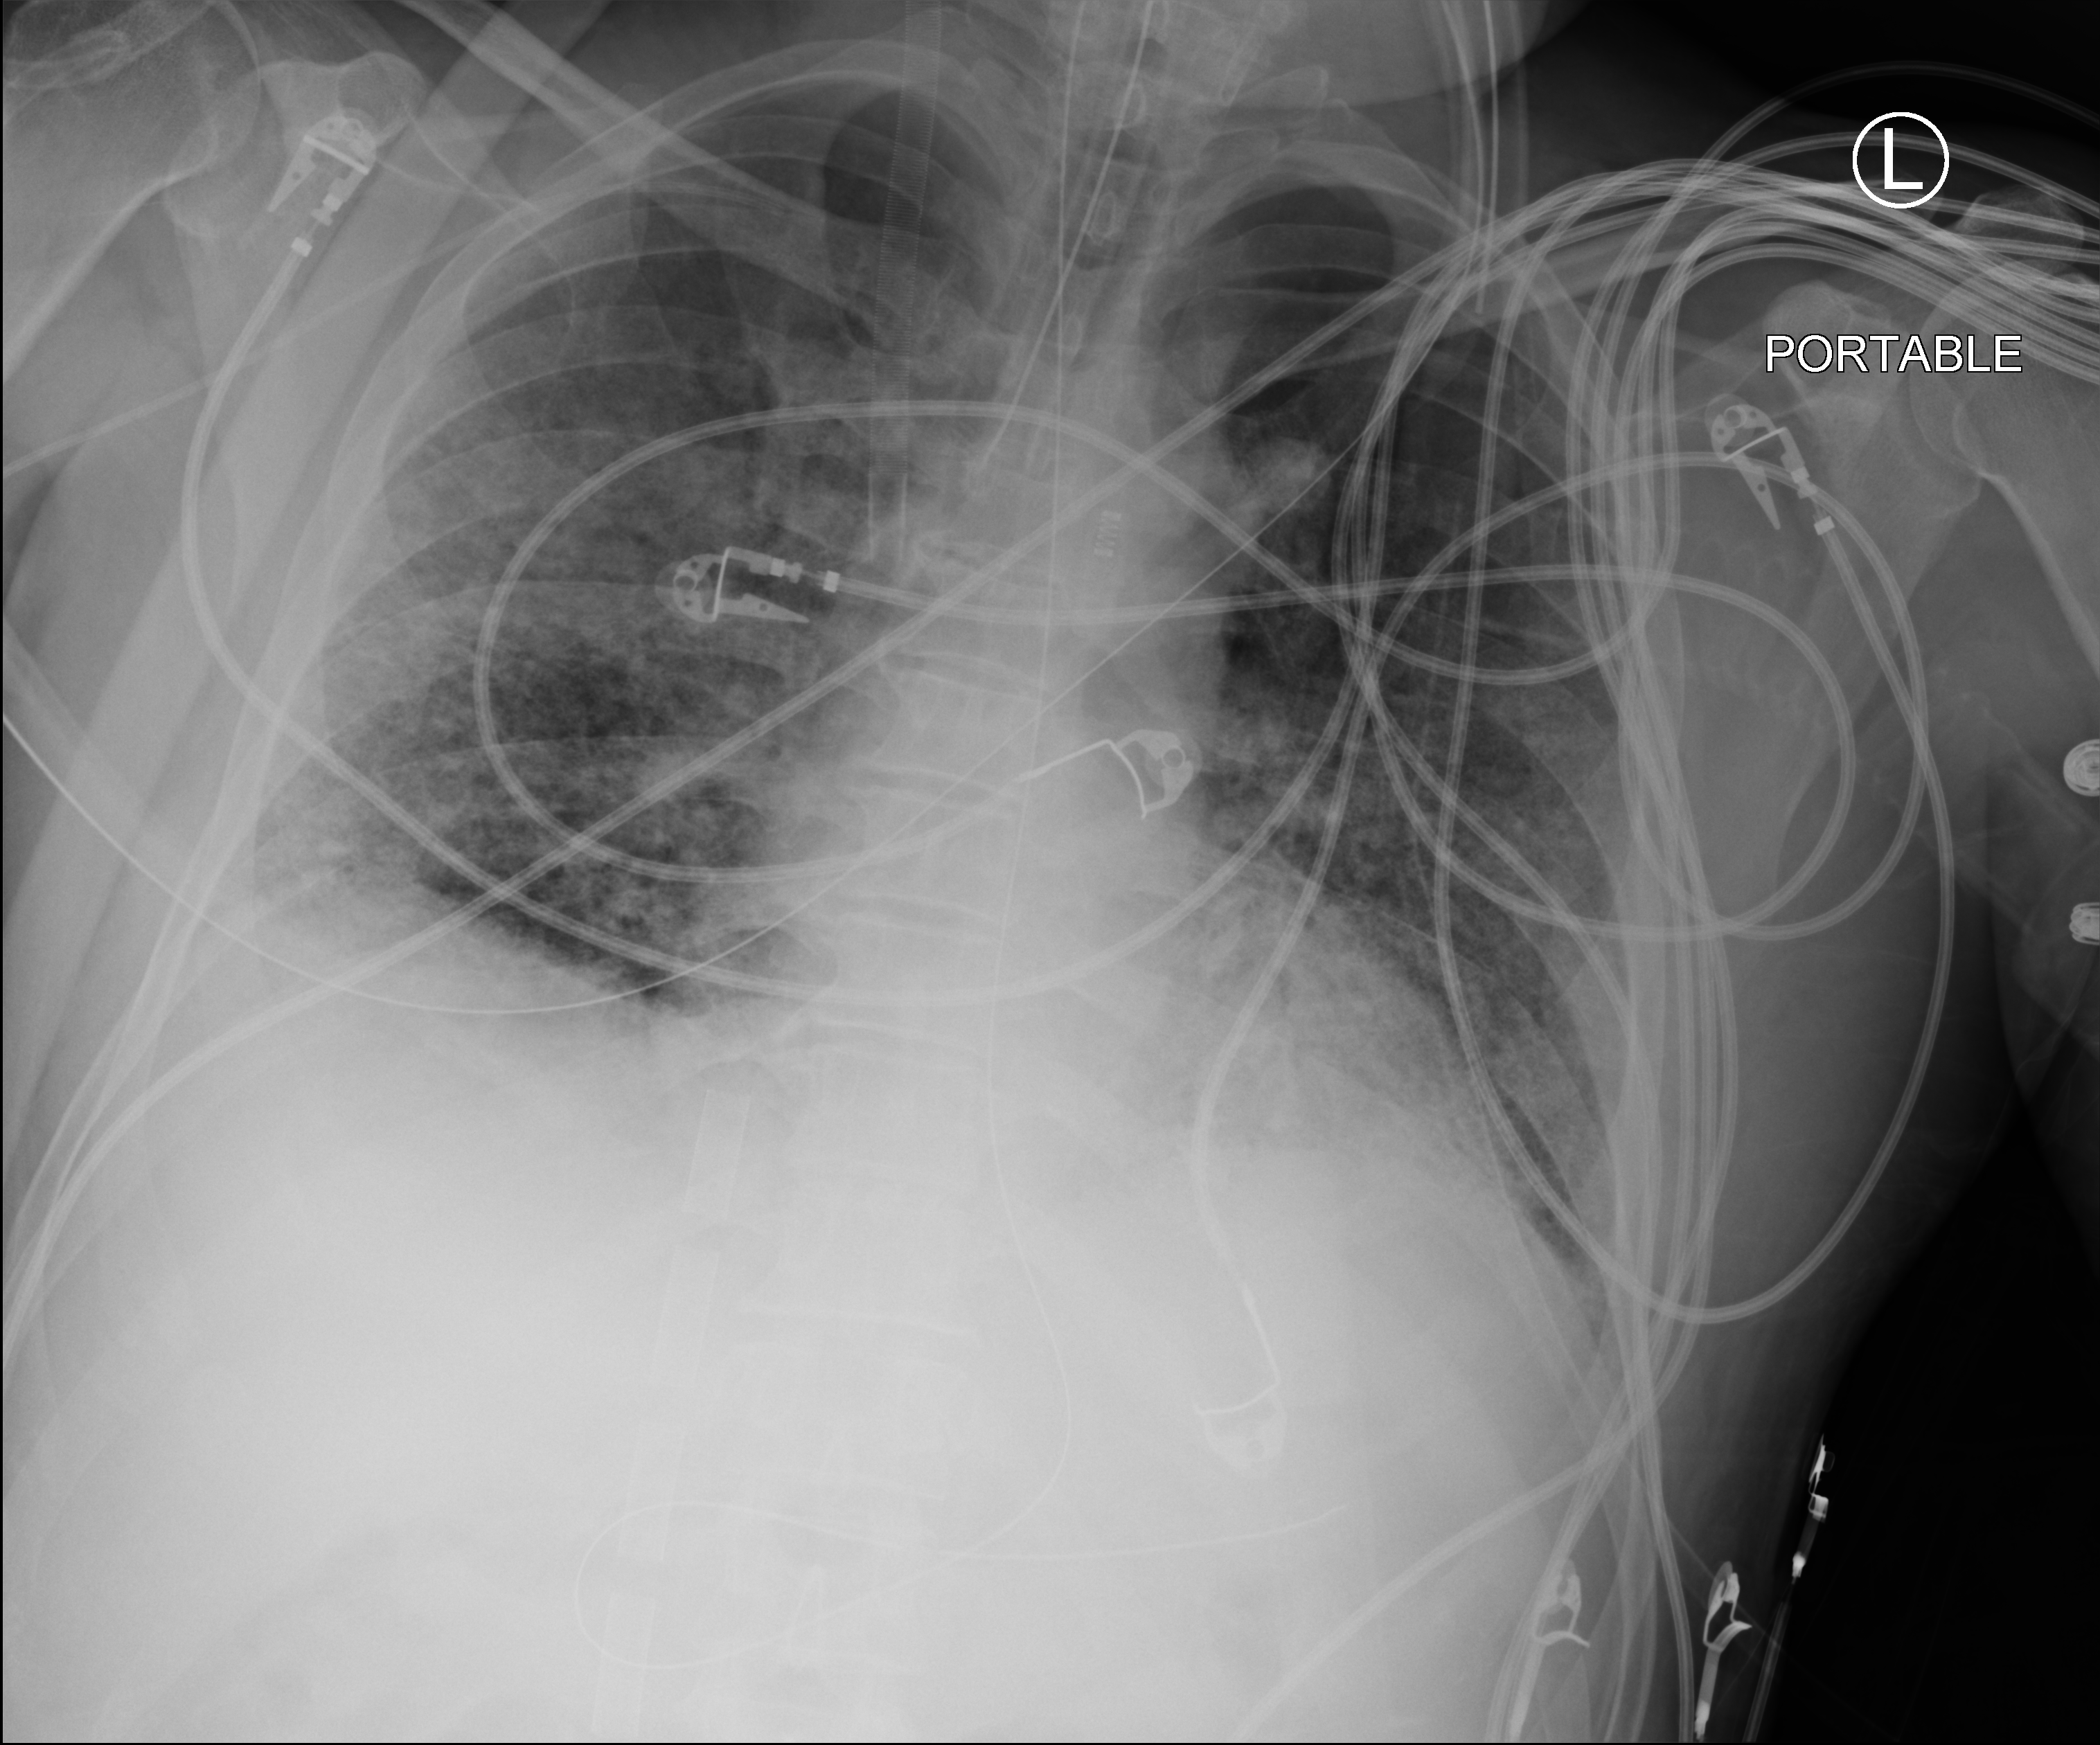
Chest X-ray (portable). Patient hospitalised with COVID-19; male, aged 18–59 years.
Admission-level facts for this patient (not findings on this image; timing relative to this image not recorded): mechanically ventilated during this hospital stay: yes.